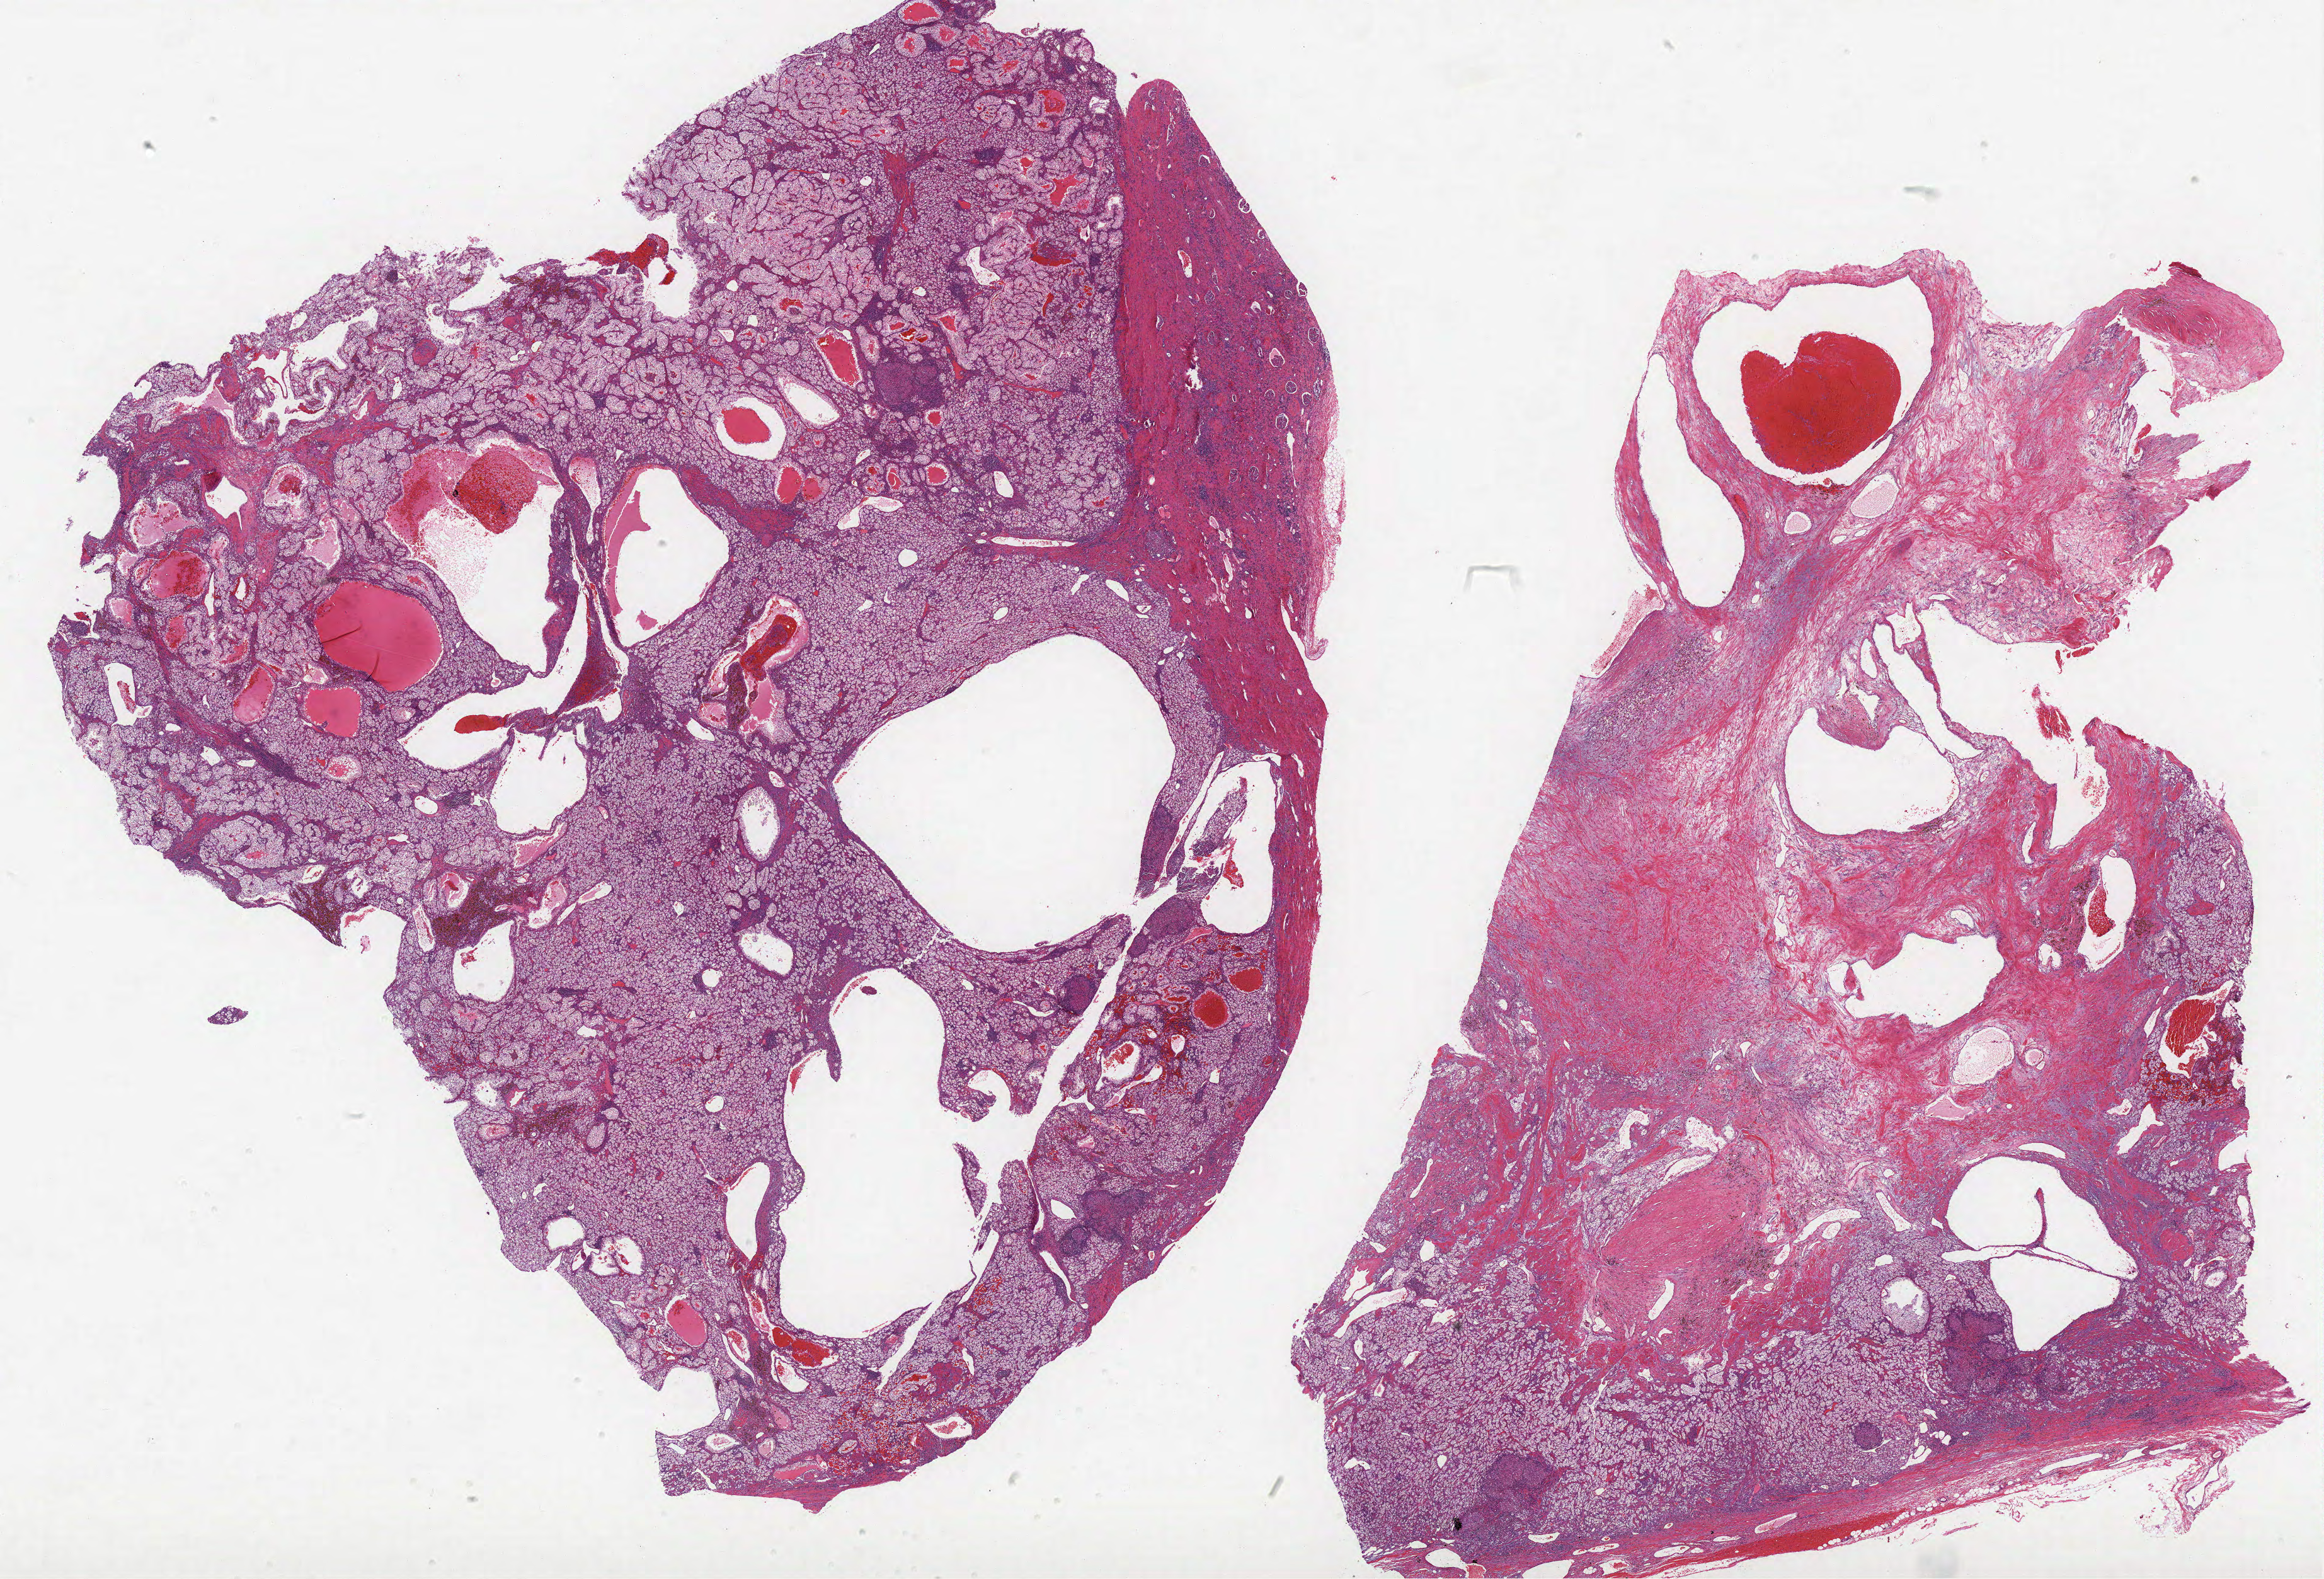
Whole-slide histology image, H&E-stained, whole scanned area (about 29.5 x 20.0 mm, slide scanned at 40x) shown as a low-resolution overview; FFPE section; sample: primary tumour, kidney. Patient: male, age at initial diagnosis 76 years. Histologic grade: G2 (moderately differentiated).
* AJCC pathologic stage: I
* histologic diagnosis: Clear cell adenocarcinoma, NOS